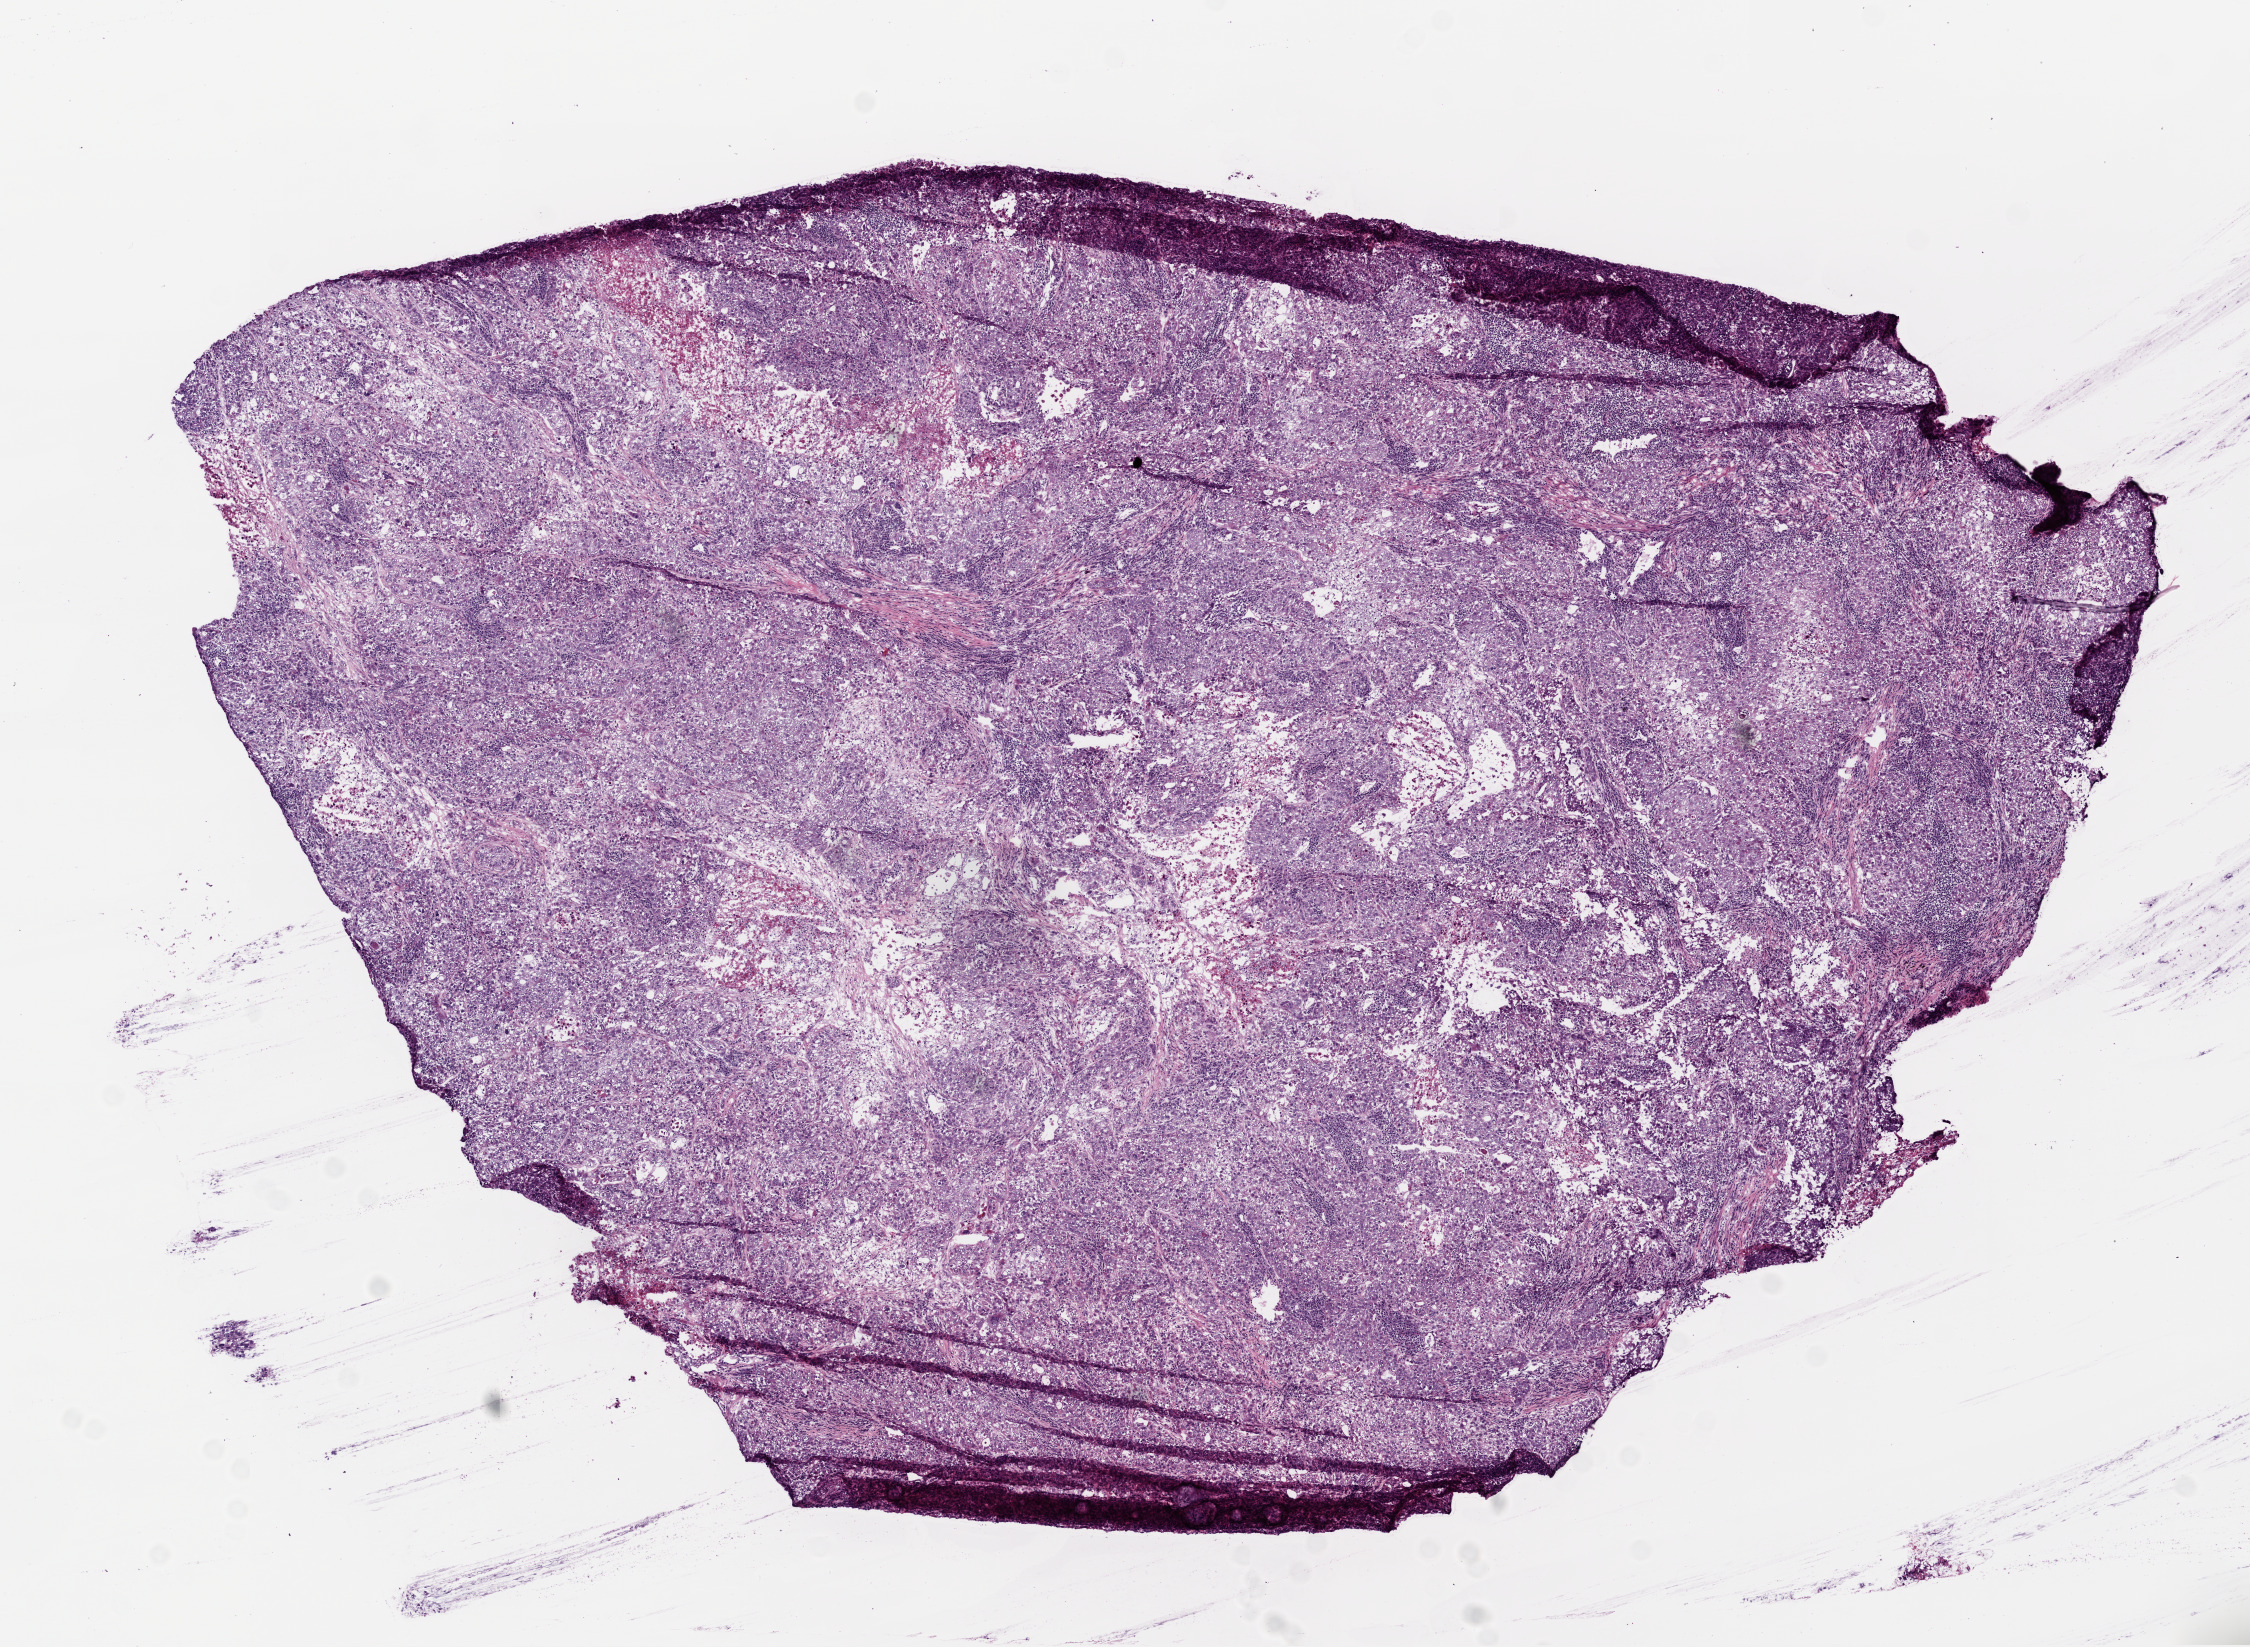
Digitized Hematoxylin and eosin (H&E) stained tissue section (whole slide), shown as a low-resolution overview of the whole scanned area (about 9.0 x 6.6 mm, slide scanned at 20x). Frozen section from the top of the tissue portion. Primary tumour sample from the lung. Male patient; age at initial diagnosis 69 years. Composition of this section per pathologist review: tumour nuclei 65%, normal cells 0%.
Histologic diagnosis: Adenocarcinoma with mixed subtypes (lower lobe, lung).